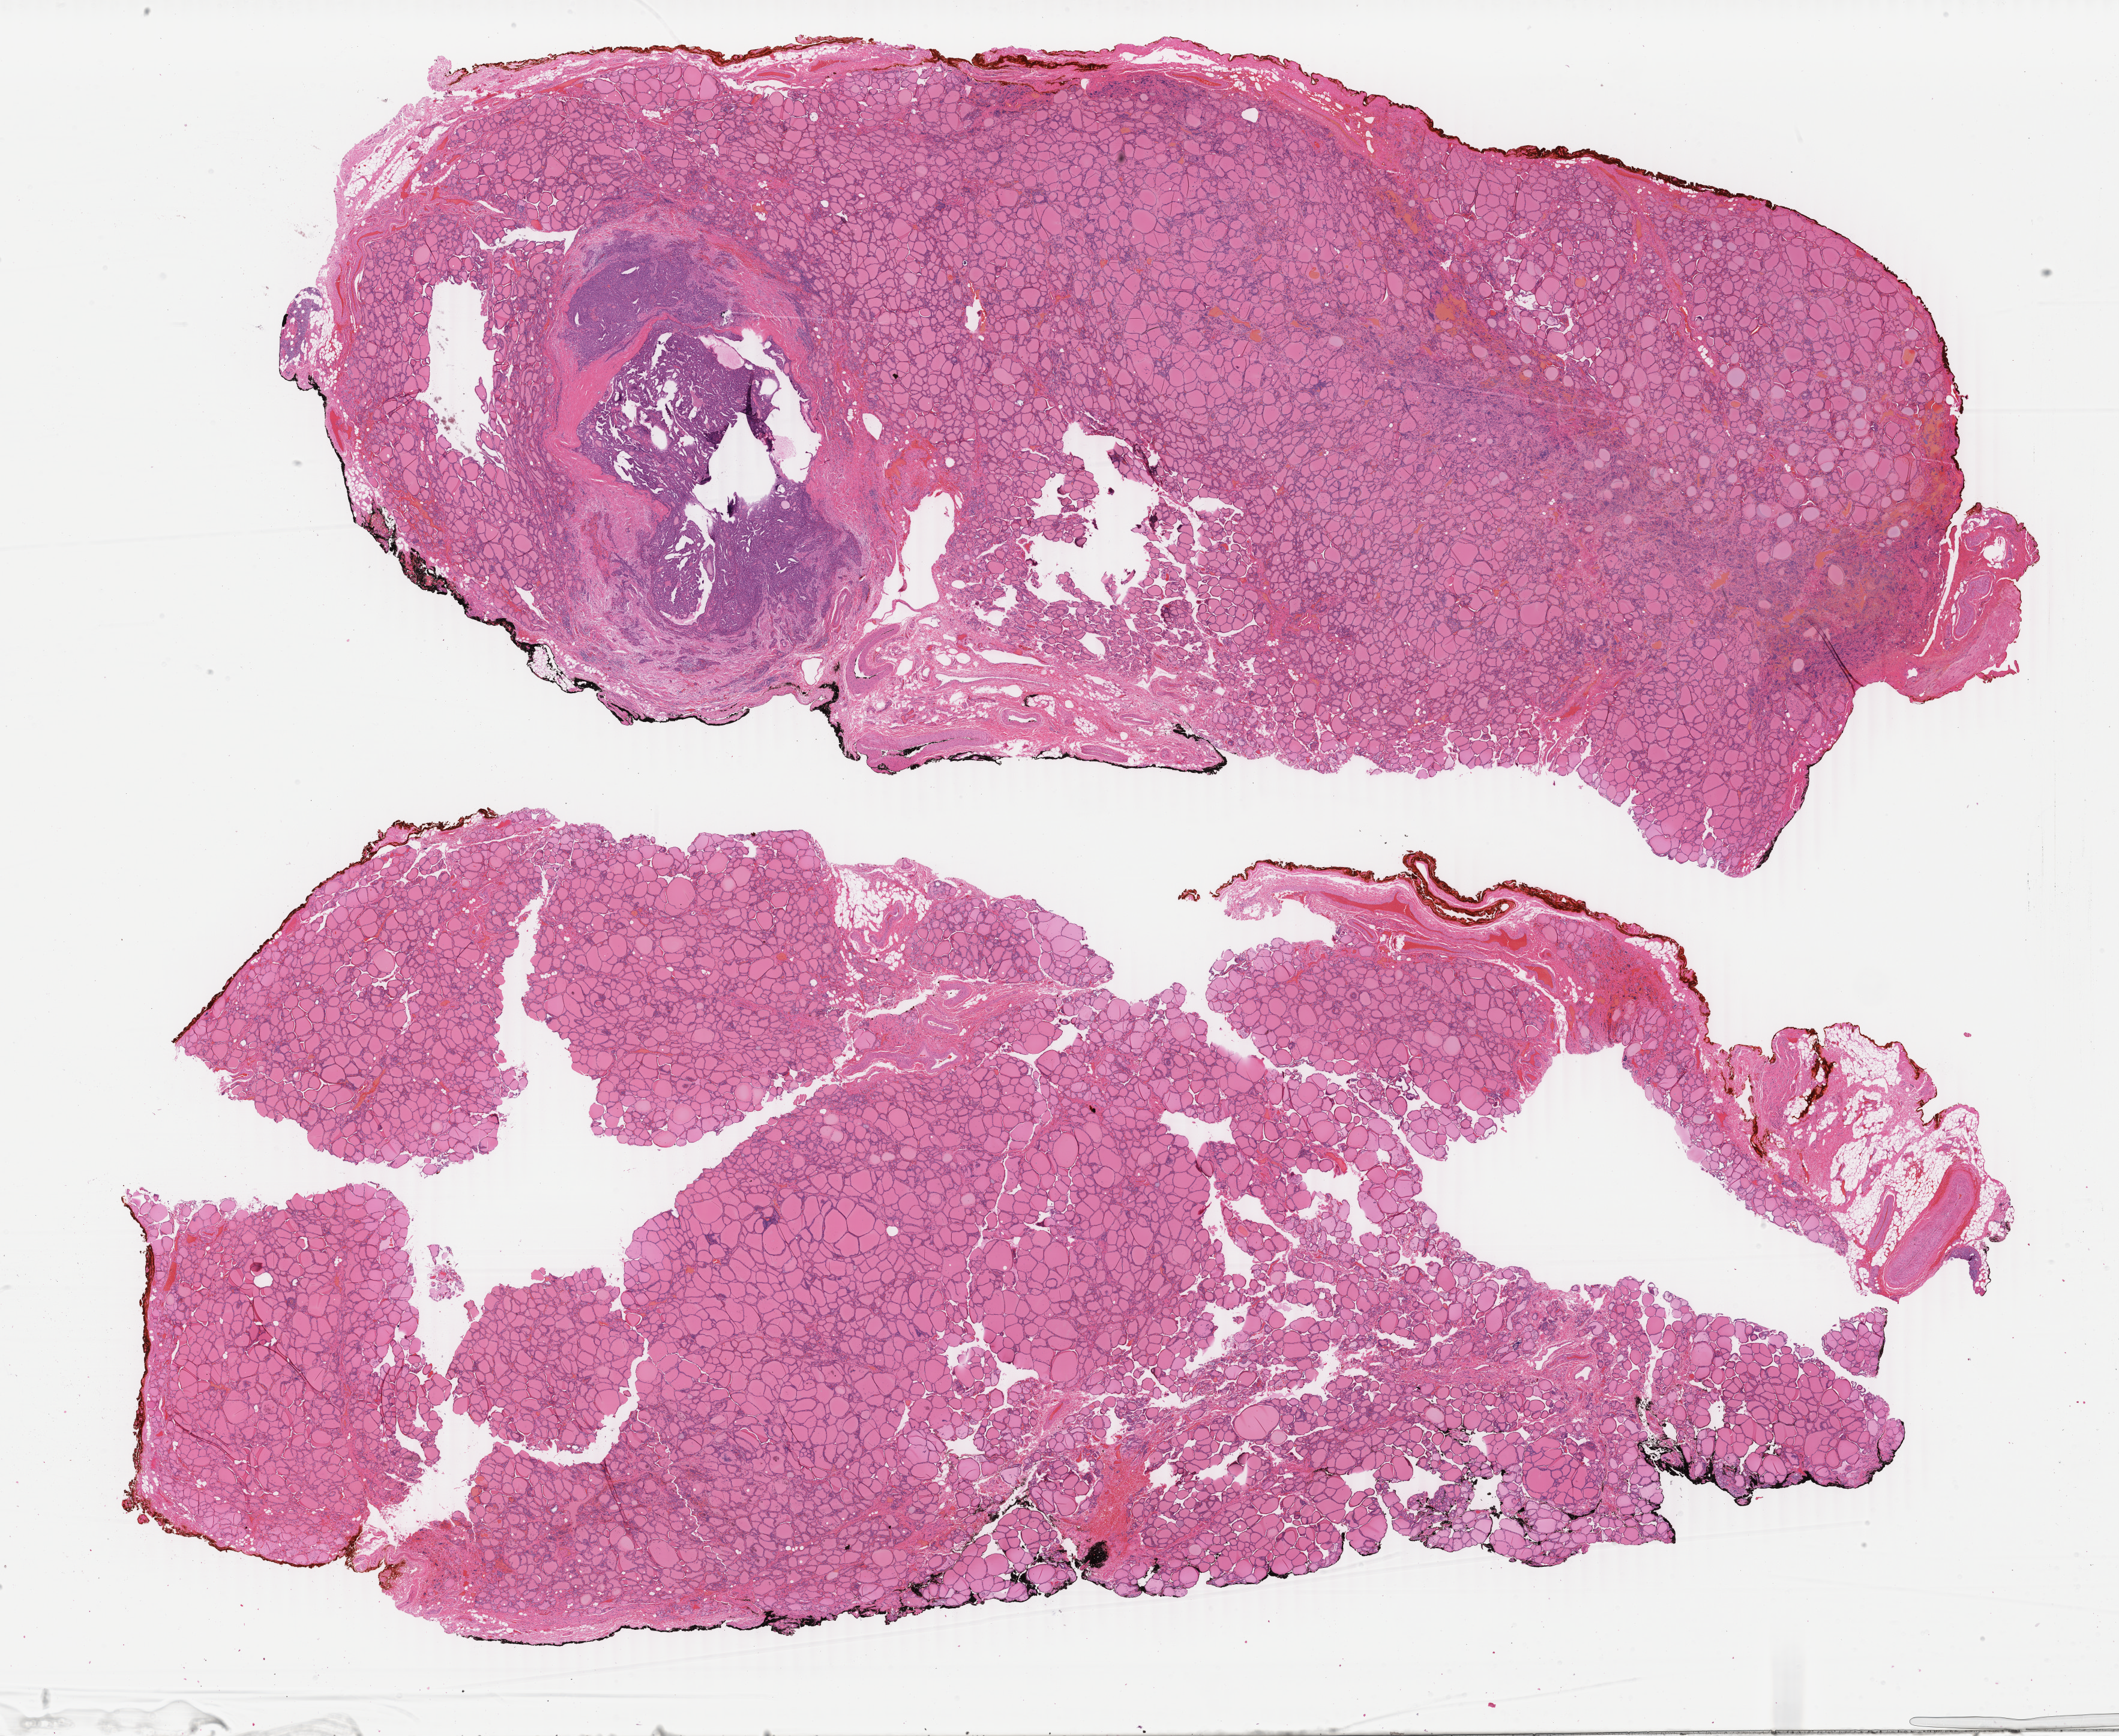
H&E whole-slide image, low-resolution overview of the scanned area, about 28.1 x 23.0 mm (acquisition: 40x scan), formalin-fixed paraffin-embedded (FFPE) diagnostic section, sample: primary tumour, thyroid. Female patient; age at initial diagnosis 40 years.
AJCC pathologic stage: I. Laterality: right. Pathologic diagnosis: Papillary adenocarcinoma, NOS (thyroid gland). Lymph nodes positive (case pathology): 2 of 18 examined.